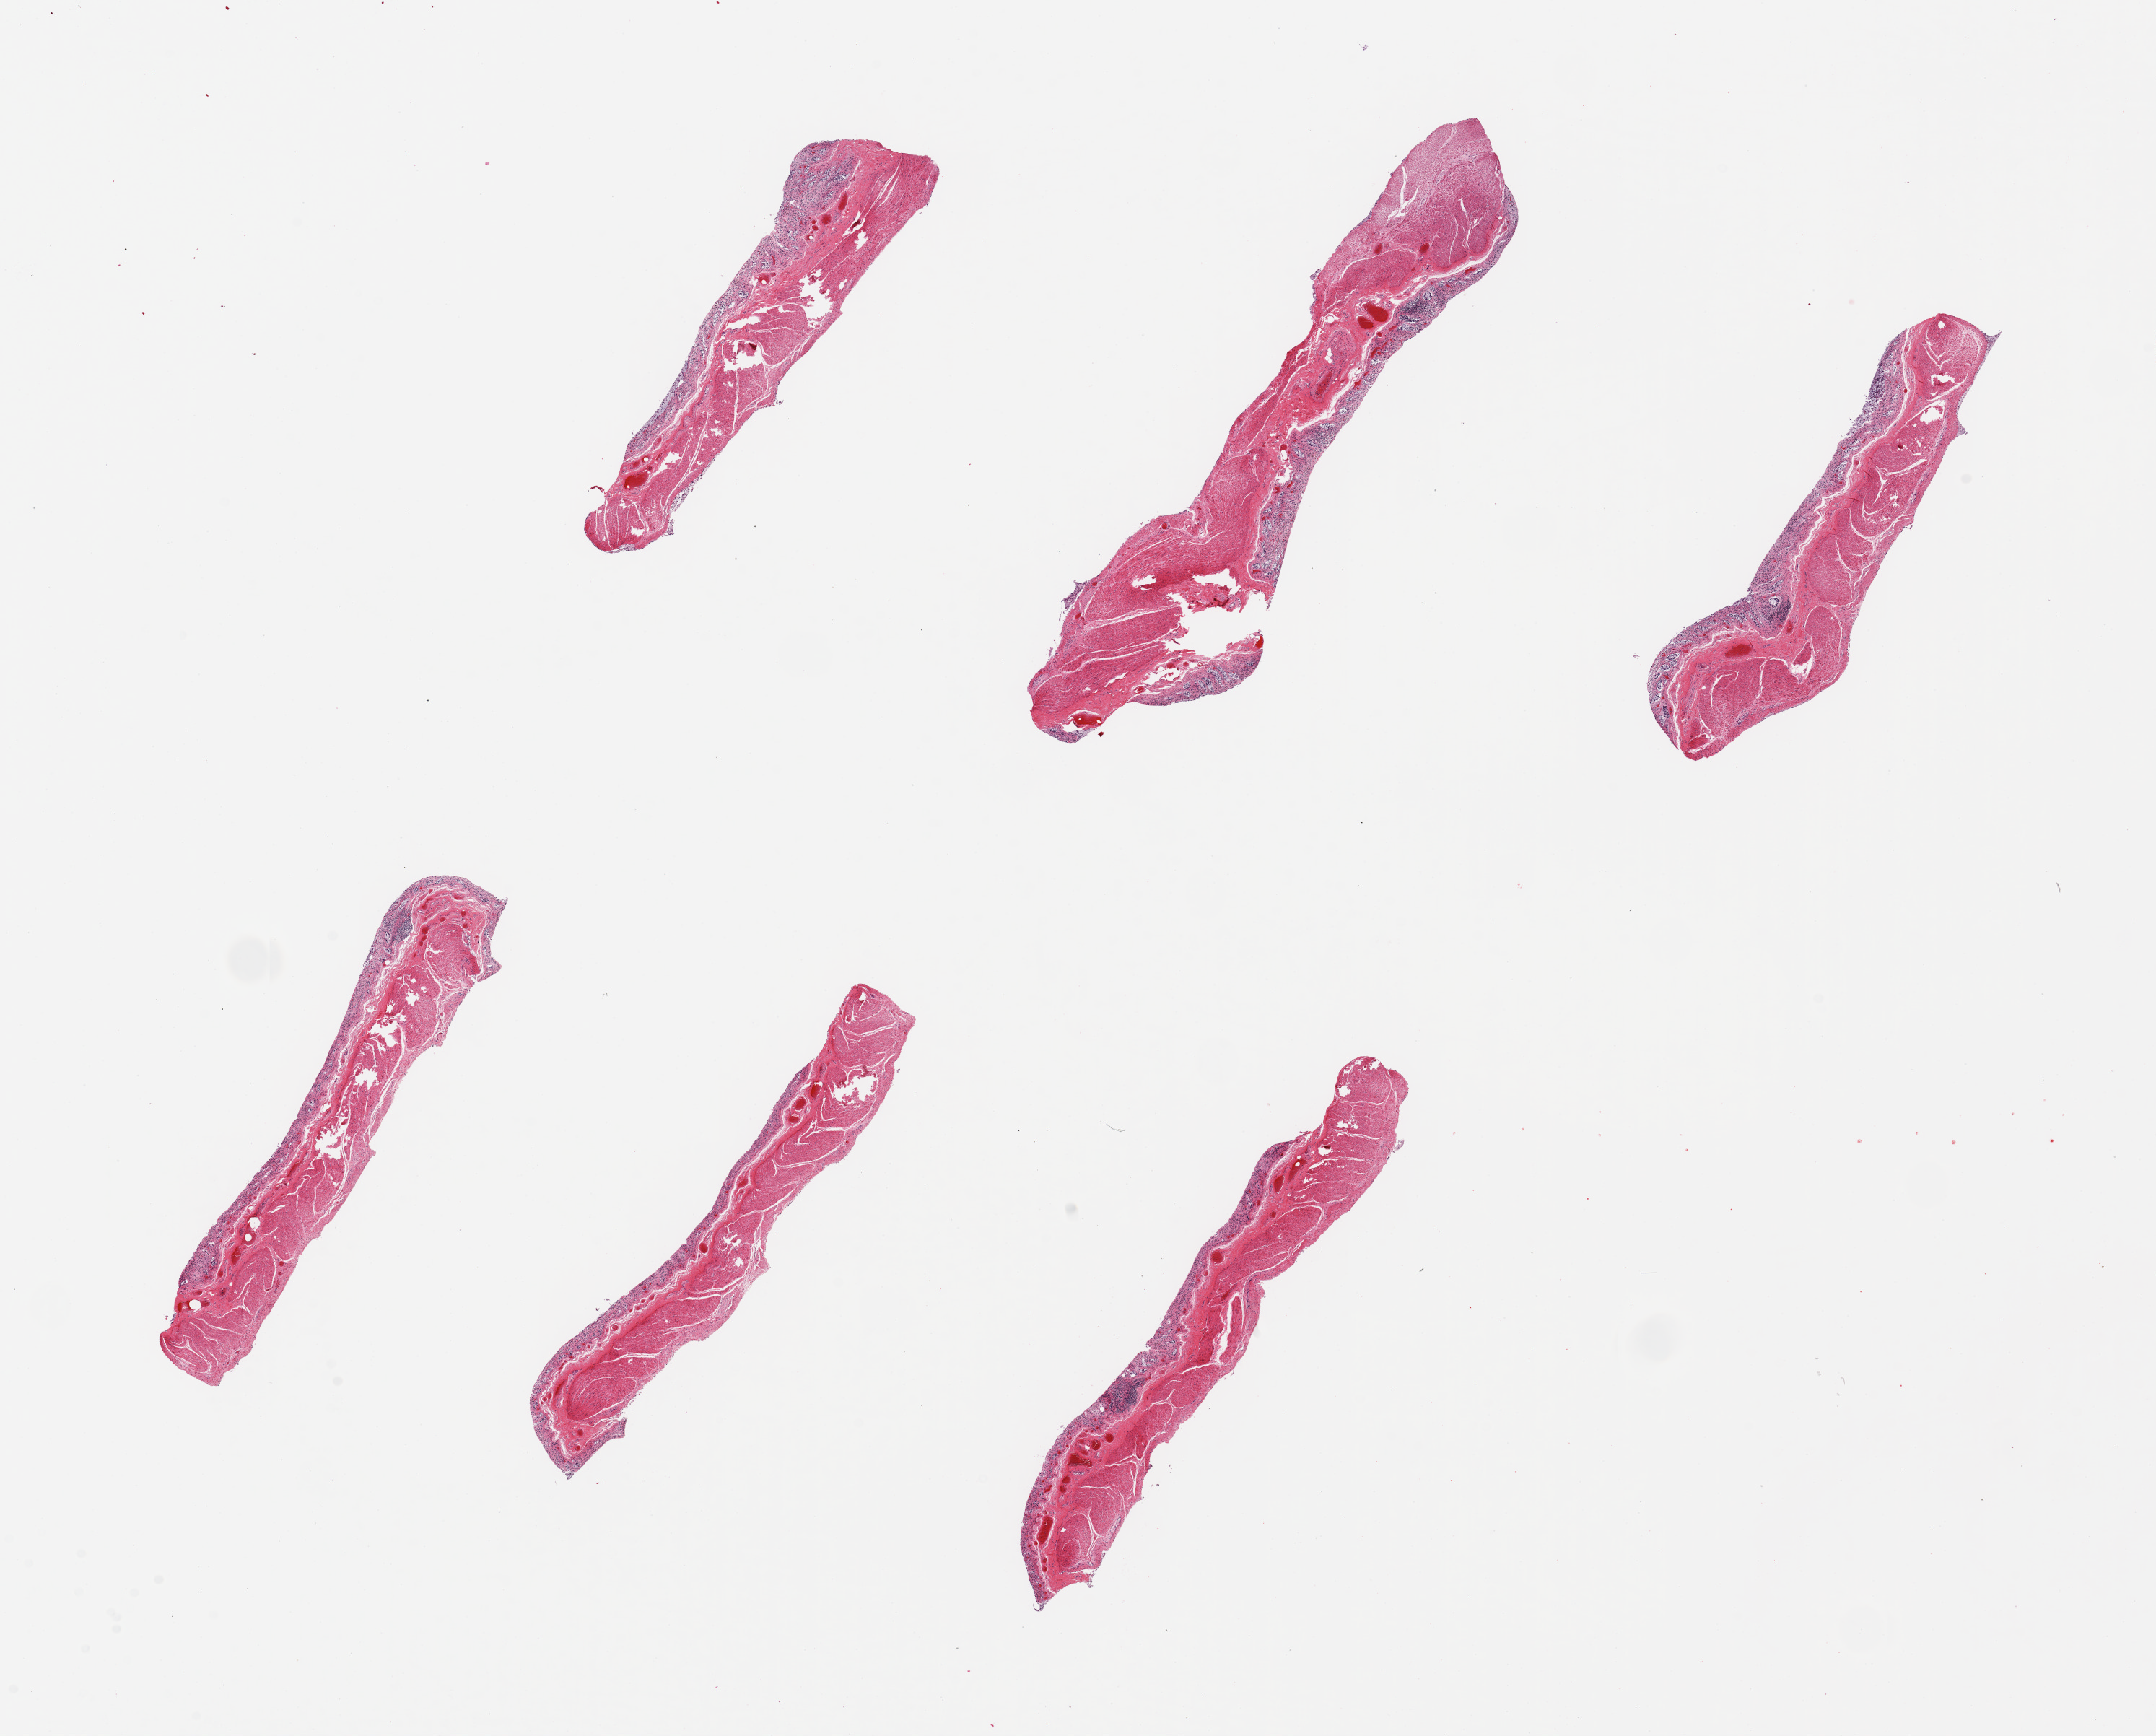
Whole-slide image, haematoxylin and eosin stain, brightfield — low-resolution overview of the scanned area, about 23.6 x 19.0 mm (slide scanned at 20x); PAXgene-fixed paraffin-embedded (PFPE) section; sampled site (target tissue): sigmoid colon; tissue donor sample. Donor: female.
Pathologist's review note for this sample: 6 pieces, up to 8x2mm; mucosa totally autolyzed; muscle in better shape.